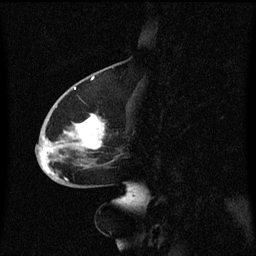
Breast MRI (dynamic contrast-enhanced), one sagittal slice. Slice 28 of 60 in the series (ordered by position). Dynamic contrast-enhanced series, image 2 of 3 at this slice position (ordered by acquisition). 1.5 T. TE 4.2 ms, TR 8.4 ms. 2 mm slice thickness. 256 × 256 image matrix. Patient: female, 68 years. From the clinical record (not read from this slice): setting: breast cancer imaged before/during neoadjuvant chemotherapy; receptor status: triple-negative.
Structures marked on this image (semi-automatically segmented with operator editing):
- analysis volume of interest (the breast-tissue region the enhancement analysis was run in; not a lesion): box from (x=36, y=94) to (x=129, y=173) px
- tumour enhancement mask (voxels above the 70 % enhancement threshold inside the analysis volume of interest): (x=41, y=114)–(x=106, y=173)